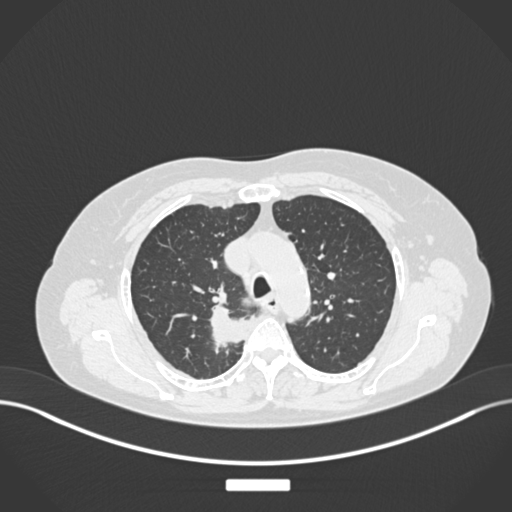
Chest CT, one axial slice. Position 189 of 237 along the scan axis. Reconstruction kernel B30f. Lung window (W 1500 / L -600 HU). 1 mm slice thickness. 512 × 512 image matrix, field of view 400 × 400 mm. Patient: female, 62 years. Case-level facts recorded for this patient, not image findings: clinical TNM (as recorded): T1c N1 M0.
Outlined on this slice (bounding box drawn by a radiologist):
- lung tumour (recorded histology: squamous cell carcinoma): bounding box [x1, y1, x2, y2] px = [208, 300, 247, 350]